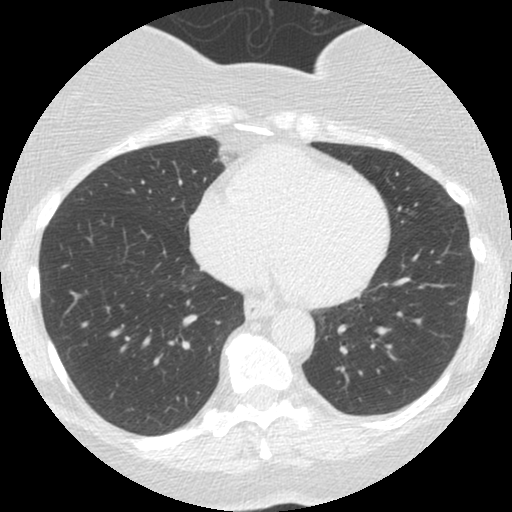
Low-dose screening chest CT, one axial slice; position 61 of 167 along the scan axis; lung window (W 1500 / L -600 HU); 2.5 mm slice thickness; 512 × 512 image matrix, field of view 300 × 300 mm.
Structures marked on this image (manually delineated by an expert):
- lesion 1 (tumor, lower lobe of left lung): bounding box [x1, y1, x2, y2] px = [398, 312, 401, 316]